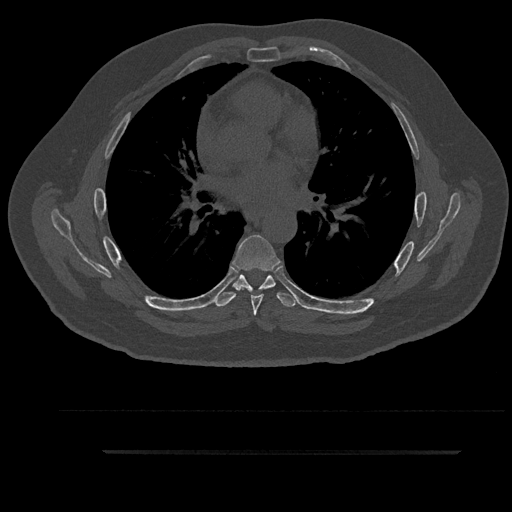
CT including the spine, one axial slice; position 556 of 797 along the scan axis; 120 kVp; bone window (W 1800 / L 400 HU); 512 × 512 image matrix, field of view 432 × 432 mm. Patient: male, 63 years. From the clinical record (not read from this slice): primary cancer: renal; vertebrae with lytic lesions (as recorded): T8.
Outlined on this slice (semi-automatically segmented with operator editing):
- T5 vertebra: bounding box (x1, y1, x2, y2) in pixels: (260, 286, 266, 289)
- T6 vertebra: (232, 235, 281, 316)
- T7 vertebra: (215, 275, 298, 307)